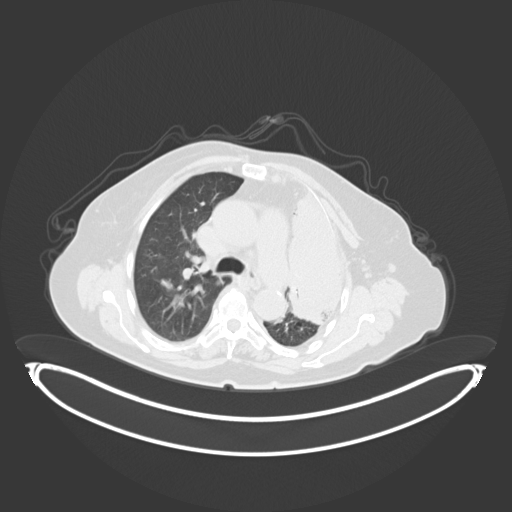
Chest CT, one axial slice. Position 211 of 284 along the scan axis. Lung window (W 1500 / L -600 HU). 3 mm slice thickness. 512 × 512 image matrix, field of view 500 × 500 mm. Female patient, age 75 years. Case-level facts recorded for this patient, not image findings: clinical TNM (as recorded): T3 N3 M1.
Outlined on this slice (rectangle marked by the reading radiologist):
- lung tumour (recorded histology: adenocarcinoma): bounding box <283,188,358,328> (left, top, right, bottom; pixels)